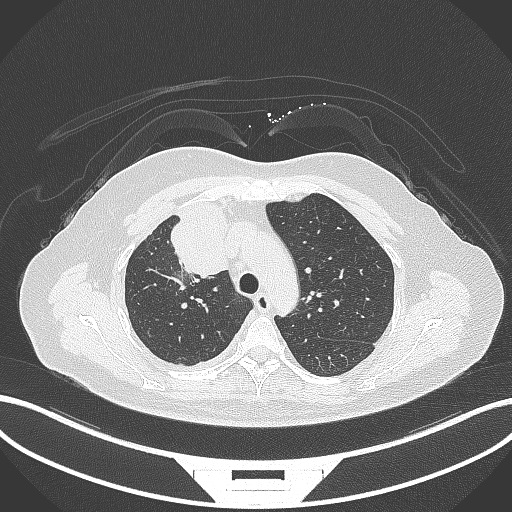
Chest CT, one axial slice; position 219 of 305 along the scan axis; lung window (W 1500 / L -600 HU); 1 mm slice thickness; 512 × 512 image matrix, field of view 400 × 400 mm. Patient: female, 52 years. Case-level facts recorded for this patient, not image findings: clinical TNM (as recorded): T3 N1 M1.
Structures marked on this image (rectangle marked by the reading radiologist):
- lung tumour (recorded histology: adenocarcinoma): bounding box (x1, y1, x2, y2) in pixels: (168, 200, 237, 278)